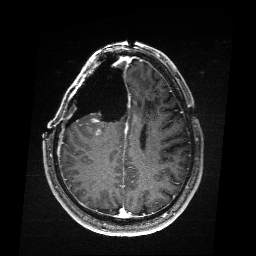
Brain MRI from a brain-tumour surgery series, one axial slice. Position 71 of 176 along the scan axis. T1-weighted post-contrast. 1 mm slice thickness. 256 × 256 image matrix. Case-level facts recorded for this patient, not image findings: histopathology: Astrocytoma; WHO grade: 4; IDH mutation: yes.
Structures marked on this image (expert manual segmentation):
- residual tumour: bounding box [x1, y1, x2, y2] px = [90, 118, 119, 135]